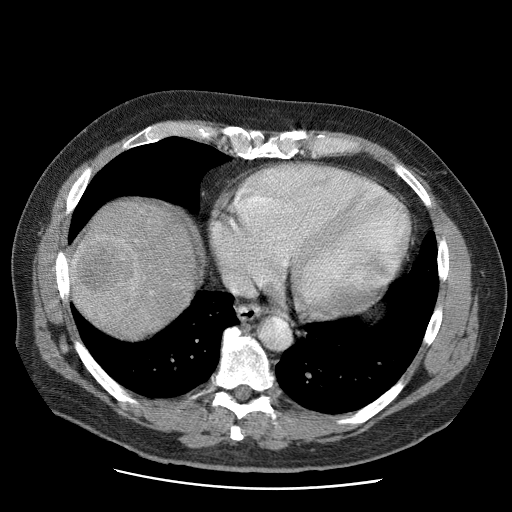
Contrast-enhanced abdominal CT (liver protocol), one axial slice. Slice 60 of 81 in the series (ordered by position). Reconstruction kernel STANDARD. 120 kVp. Soft-tissue window (W 400 / L 40 HU). 2.5 mm slice thickness. 512 × 512 image matrix, field of view 380 × 380 mm. From the clinical record (not read from this slice): diagnosis: hepatocellular carcinoma (patient treated with transarterial chemoembolisation; whether this scan precedes or follows treatment is not stated here); TNM stage (as recorded): Stage-IIIA; Child-Pugh class: A; tumour differentiation: moderately differentiated; tumour nodularity: multinodular.
Annotated regions visible in this slice (semi-automatic segmentation, software-assisted and operator-edited):
- liver parenchyma outside the tumour (the mass and vessels are separate outlines, so this box may not span the whole liver): bounding box <68,200,198,336> (left, top, right, bottom; pixels)
- mass: <68,231,145,324>